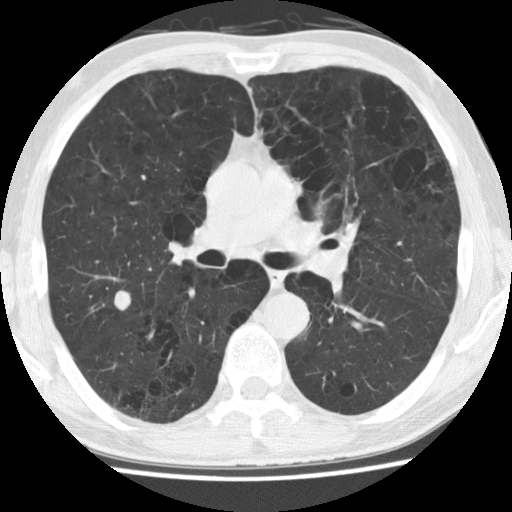
Low-dose screening chest CT, one axial slice. Position 89 of 158 along the scan axis. Reconstruction kernel STANDARD. 120 kVp. Lung window (W 1500 / L -600 HU). 2.5 mm slice thickness. 512 × 512 image matrix, field of view 324 × 324 mm.
Outlined on this slice (expert manual segmentation):
- lesion 1 (tumor, upper lobe of right lung): bounding box [x1, y1, x2, y2] px = [114, 290, 131, 311]